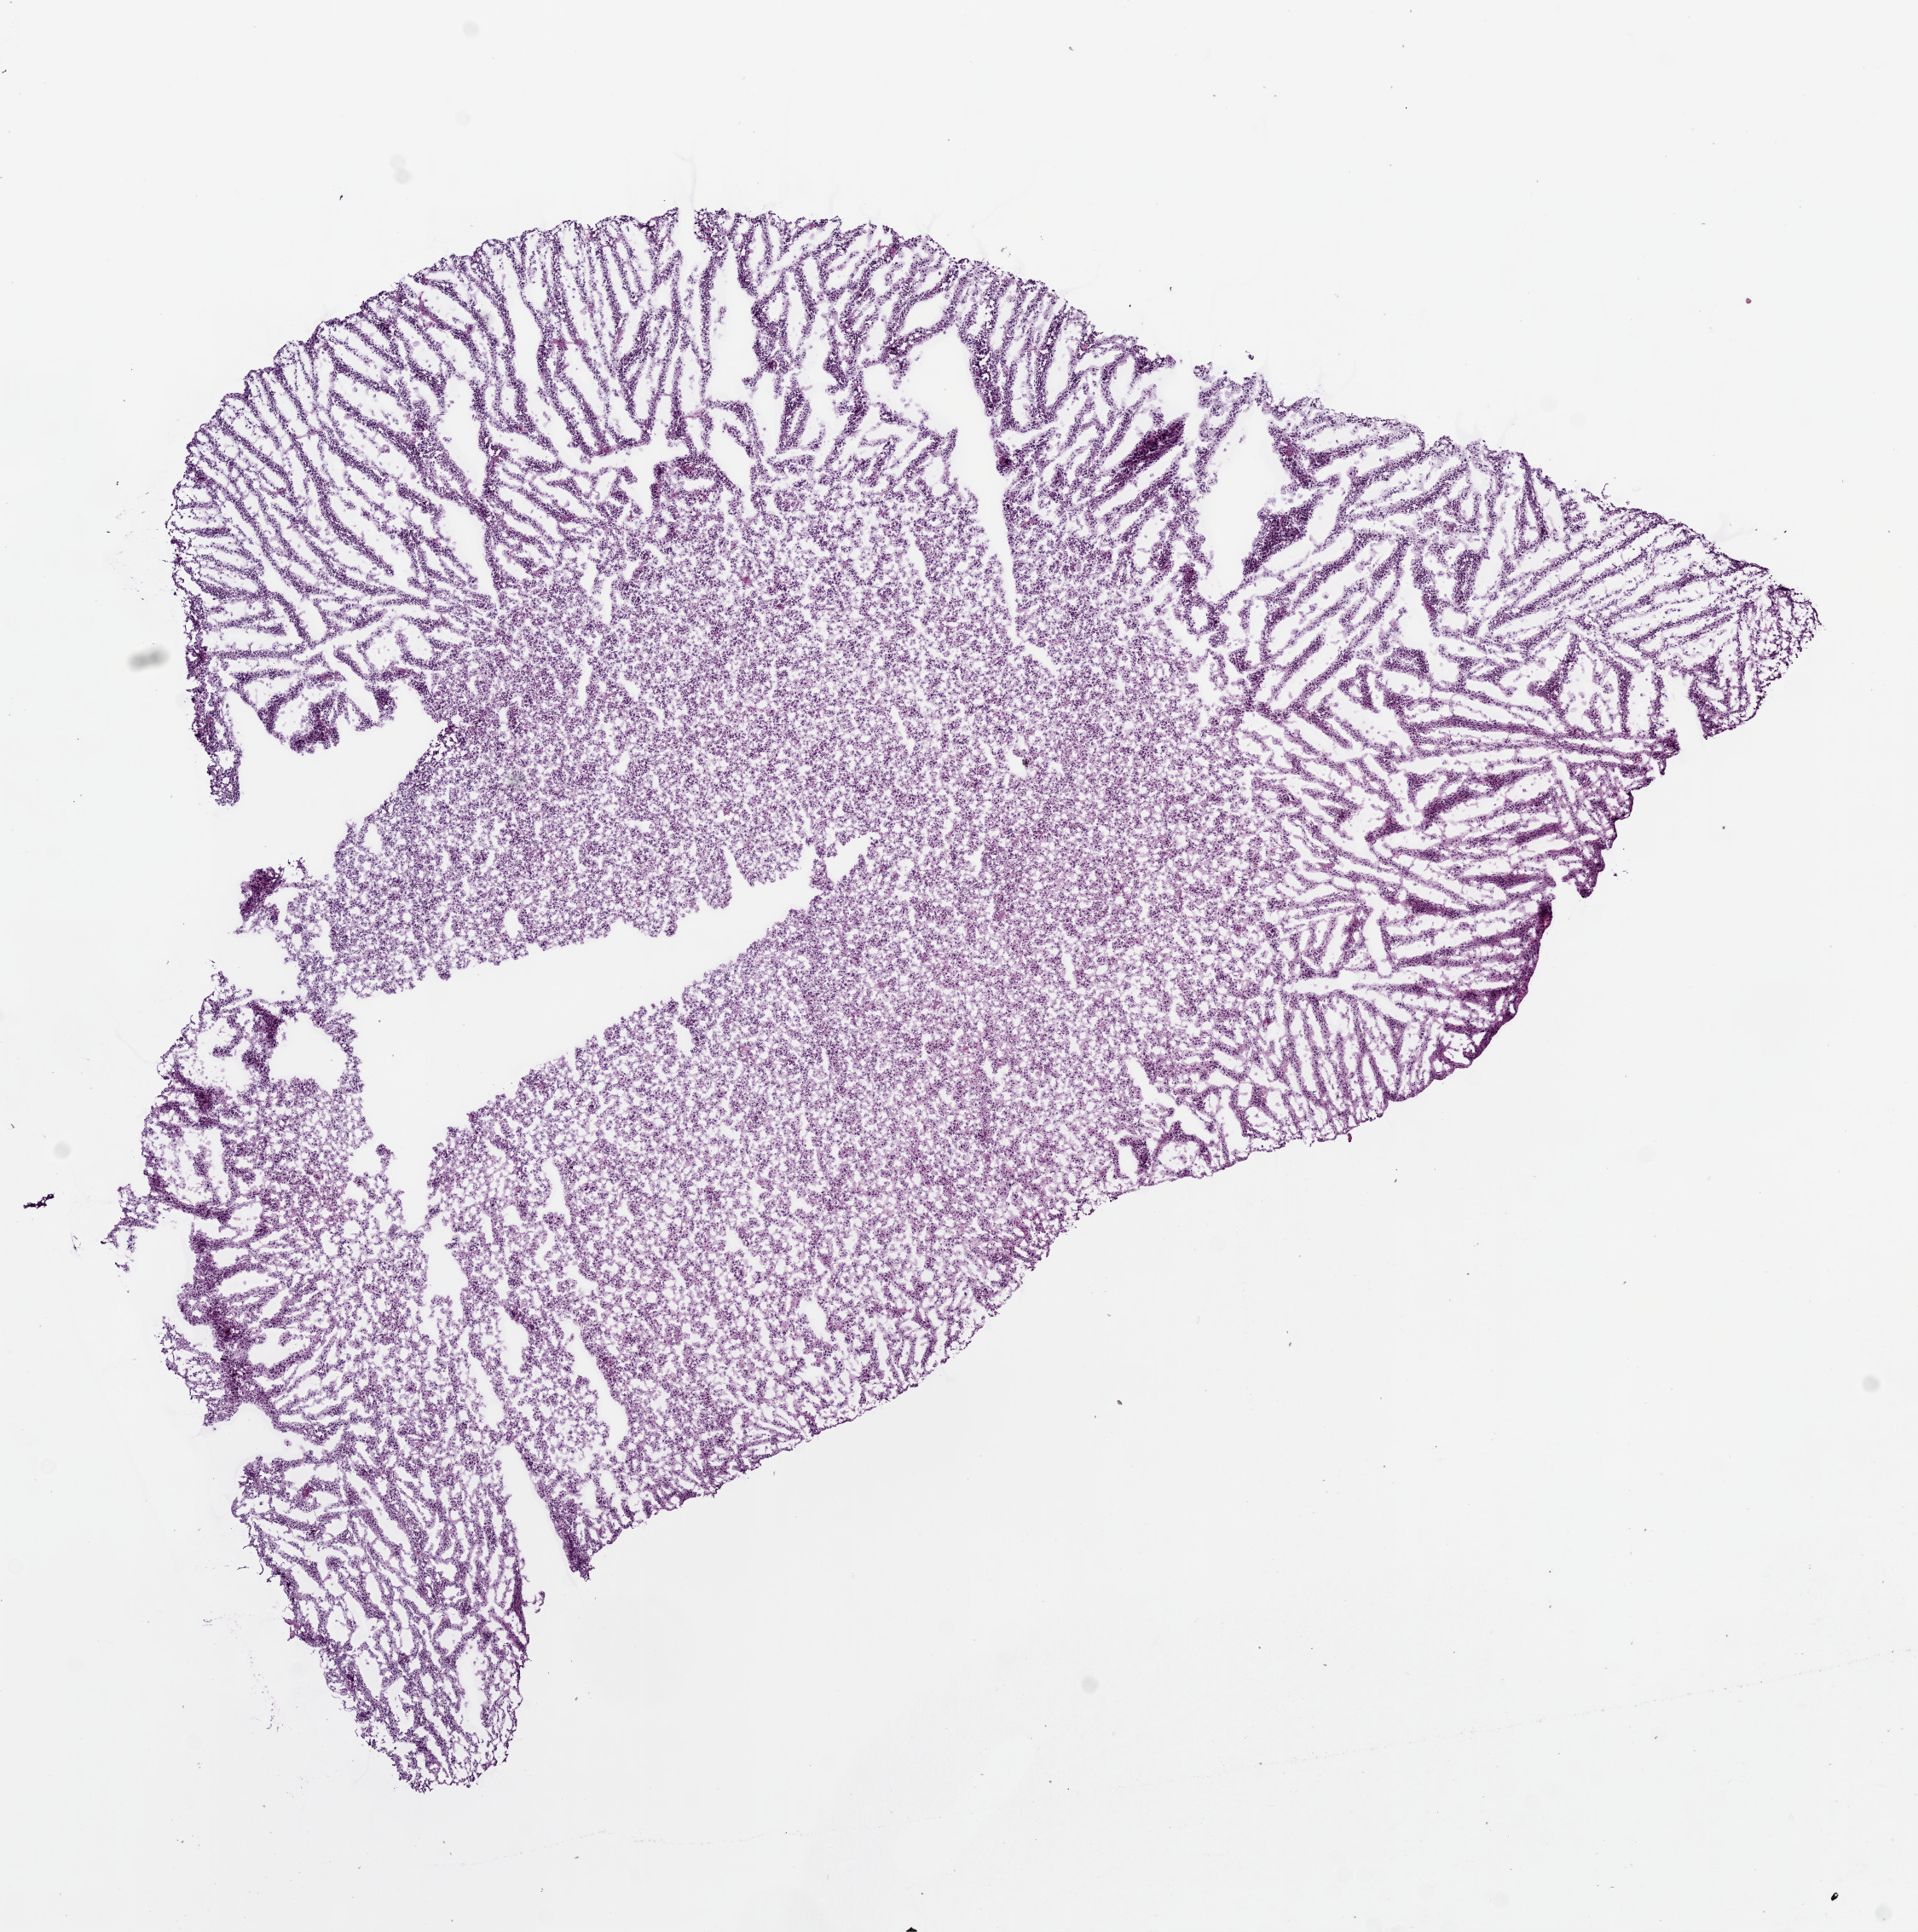
Whole-slide histology image, Hematoxylin and eosin (H&E) stained — a low-resolution overview of the entire scanned area, about 9.0 x 9.1 mm. Frozen section. Brain, primary tumour sample. Male, age 42 years at initial diagnosis. Histologic grade: G3 (poorly differentiated). Composition of this section per pathologist review: tumour cells 100%, tumour nuclei 80%, normal cells 0%, stromal cells 0%, necrosis 0%.
Pathologic diagnosis: Astrocytoma, anaplastic.